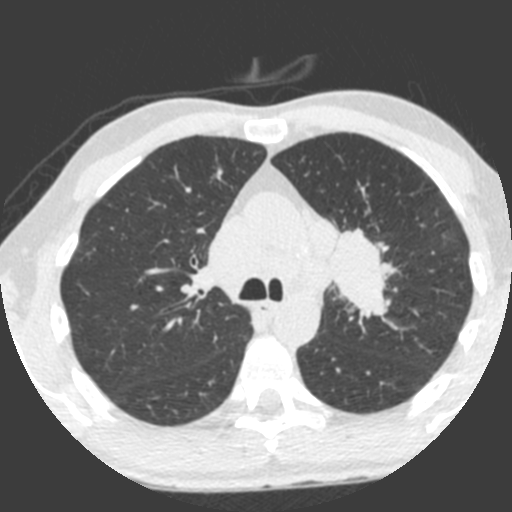
Low-dose screening chest CT, one axial slice. Position 147 of 212 along the scan axis. 120 kVp. Lung window (W 1500 / L -600 HU). 2 mm slice thickness. 512 × 512 image matrix, field of view 315 × 315 mm.
Structures marked on this image (expert manual segmentation):
- lesion 1 (tumor, upper lobe of left lung): box from (x=330, y=228) to (x=396, y=320) px